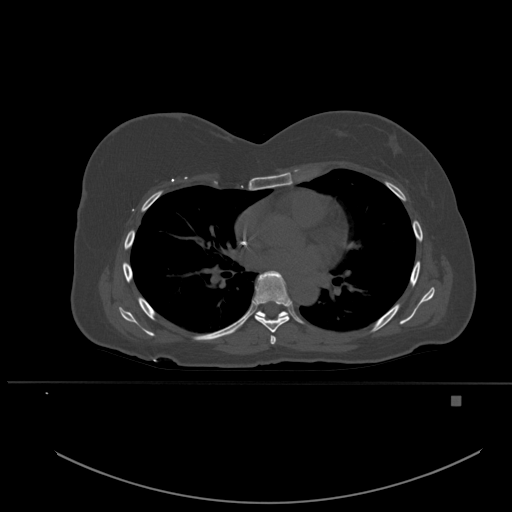
CT including the spine, one axial slice. Slice 346 of 651 in the series (ordered by position). Bone window (W 1800 / L 400 HU). 1.5 mm slice thickness. 512 × 512 image matrix, field of view 443 × 443 mm. Patient: female, 49 years. From the clinical record (not read from this slice): primary cancer: breast; vertebrae with lytic lesions (as recorded): L3, T12, L4.
Outlined on this slice (semi-automatically segmented with operator editing):
- T5 vertebra: bounding box (x1, y1, x2, y2) in pixels: (270, 335, 276, 344)
- T6 vertebra: (253, 270, 291, 333)
- T7 vertebra: (256, 310, 288, 318)